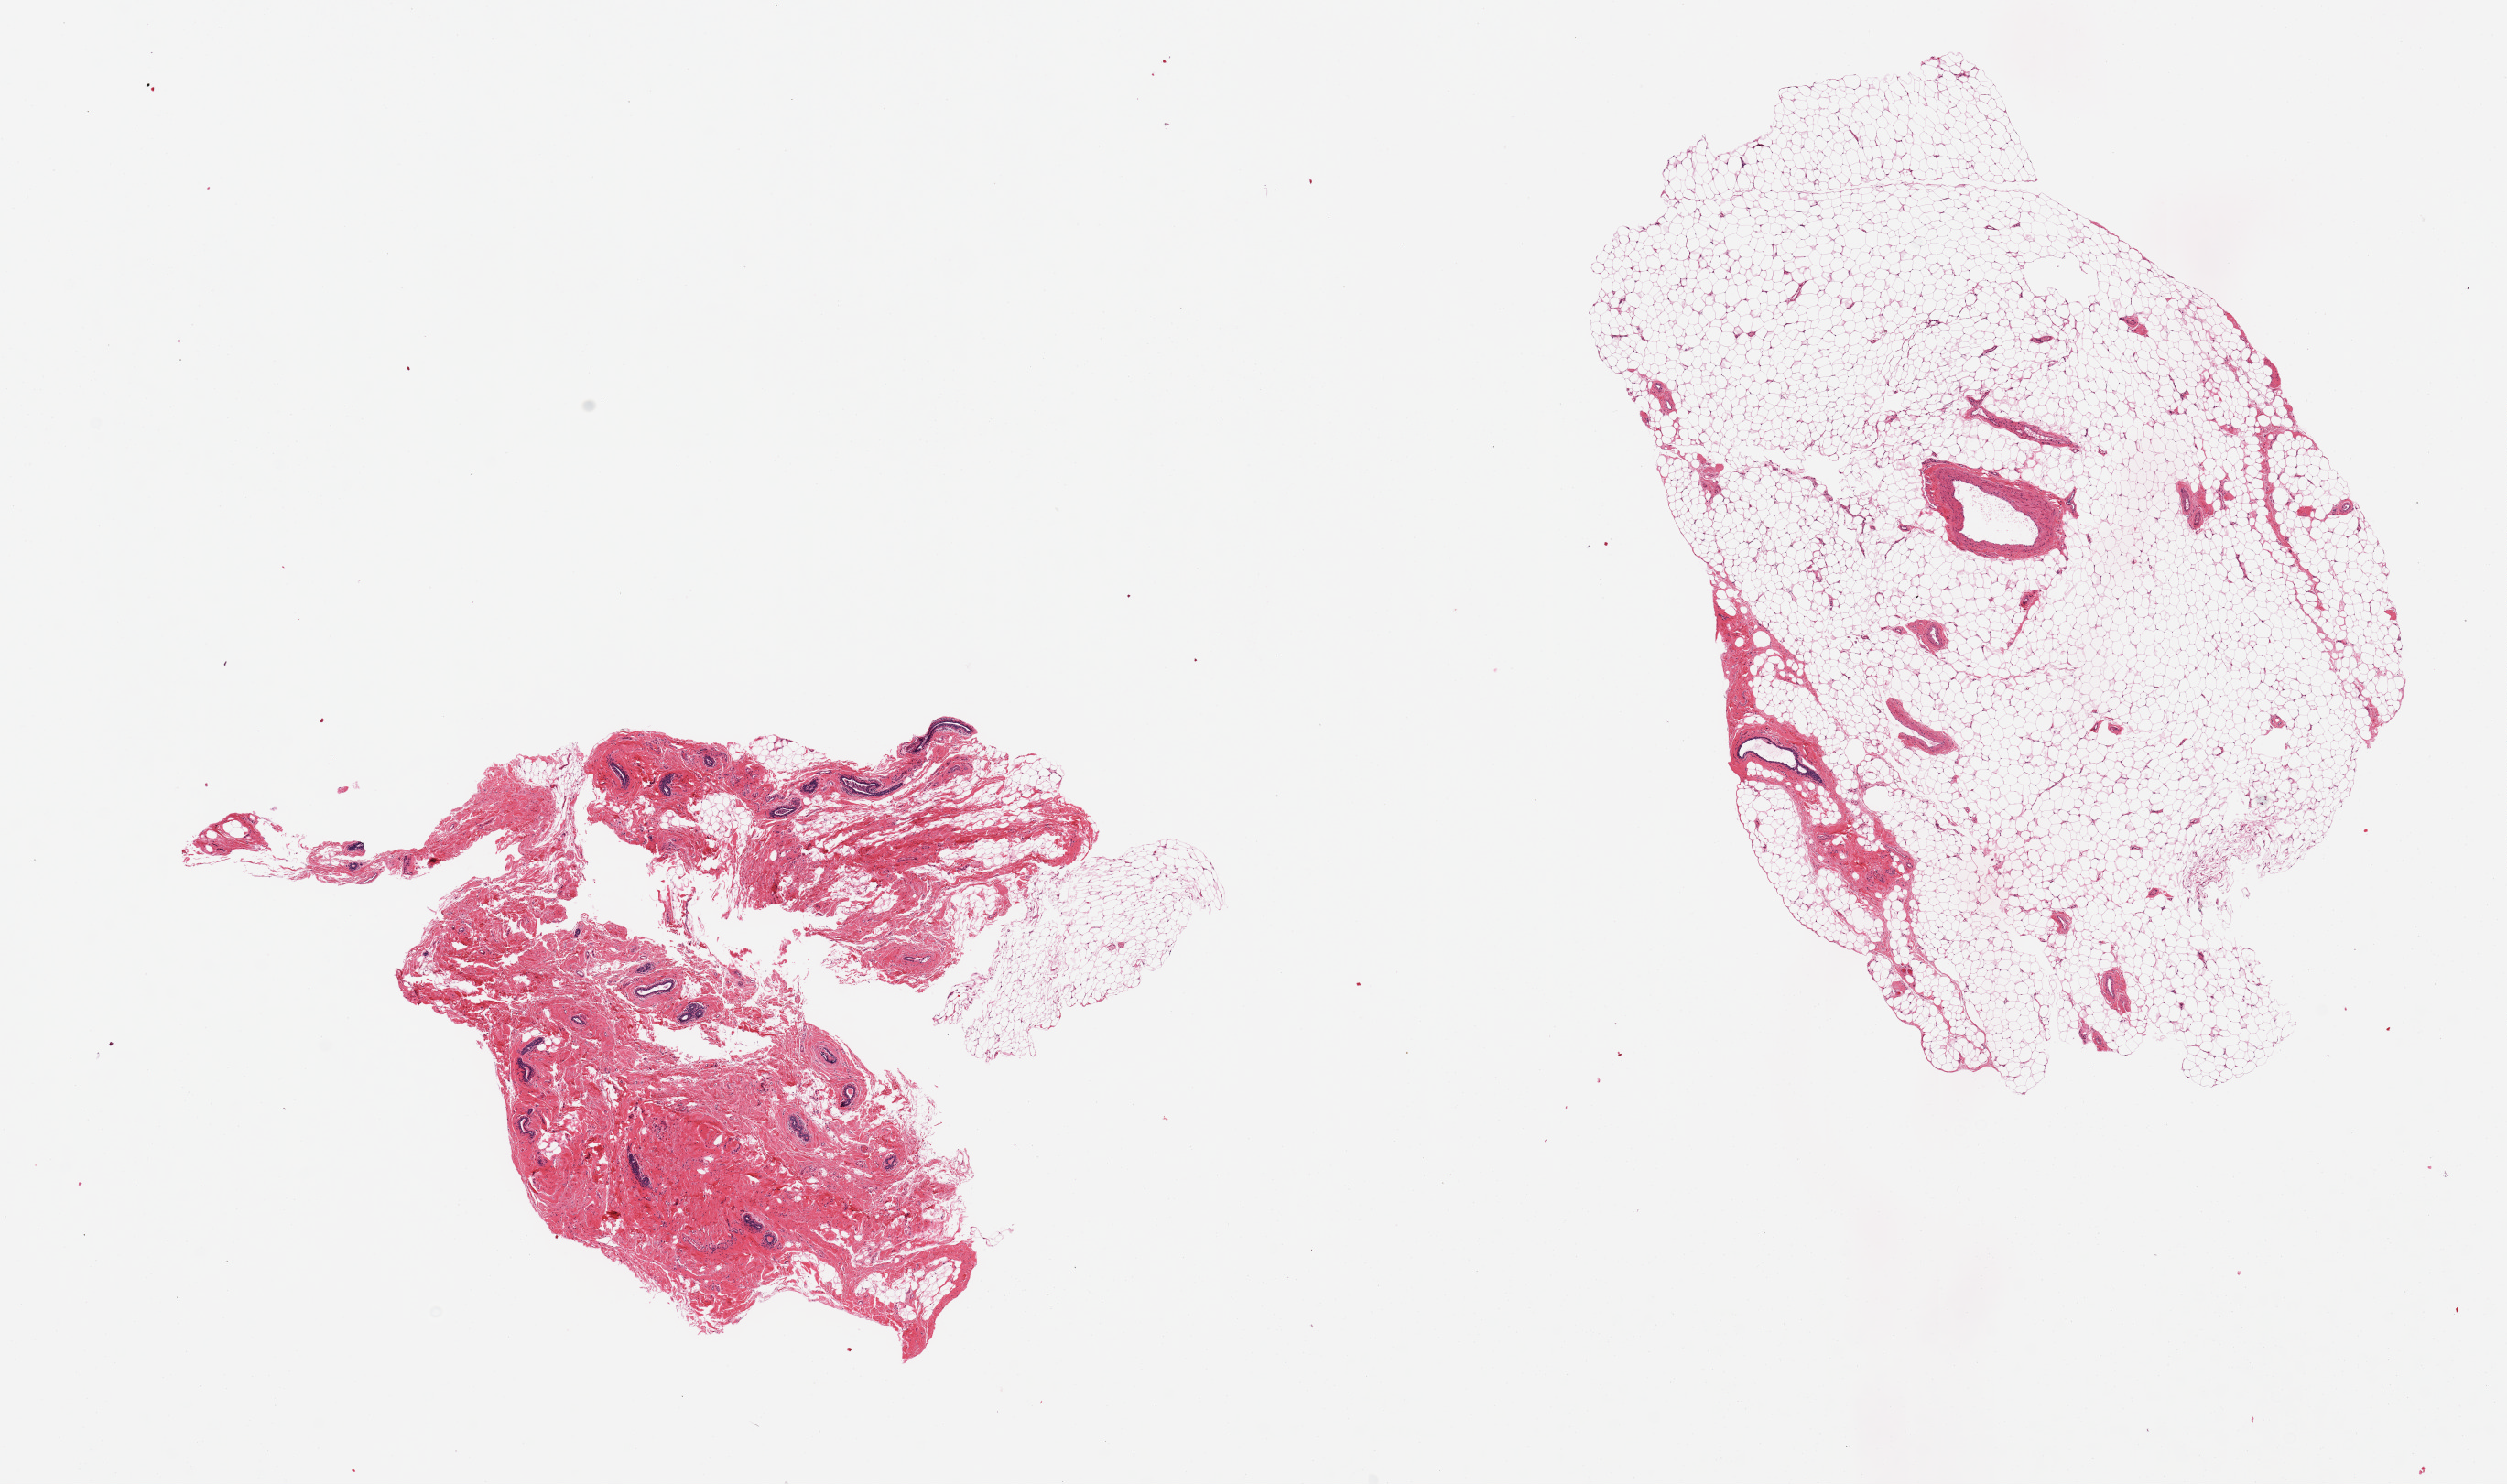
Haematoxylin and eosin whole-slide image, a low-resolution overview of the entire scanned area, about 21.7 x 12.8 mm (slide scanned at 20x), PAXgene-fixed, paraffin-embedded tissue, section of breast (target tissue), donor tissue sample.
Review note (as recorded): 2 pieces, trace inactive ductal units noted; Mainly adipose/stromal tissue.